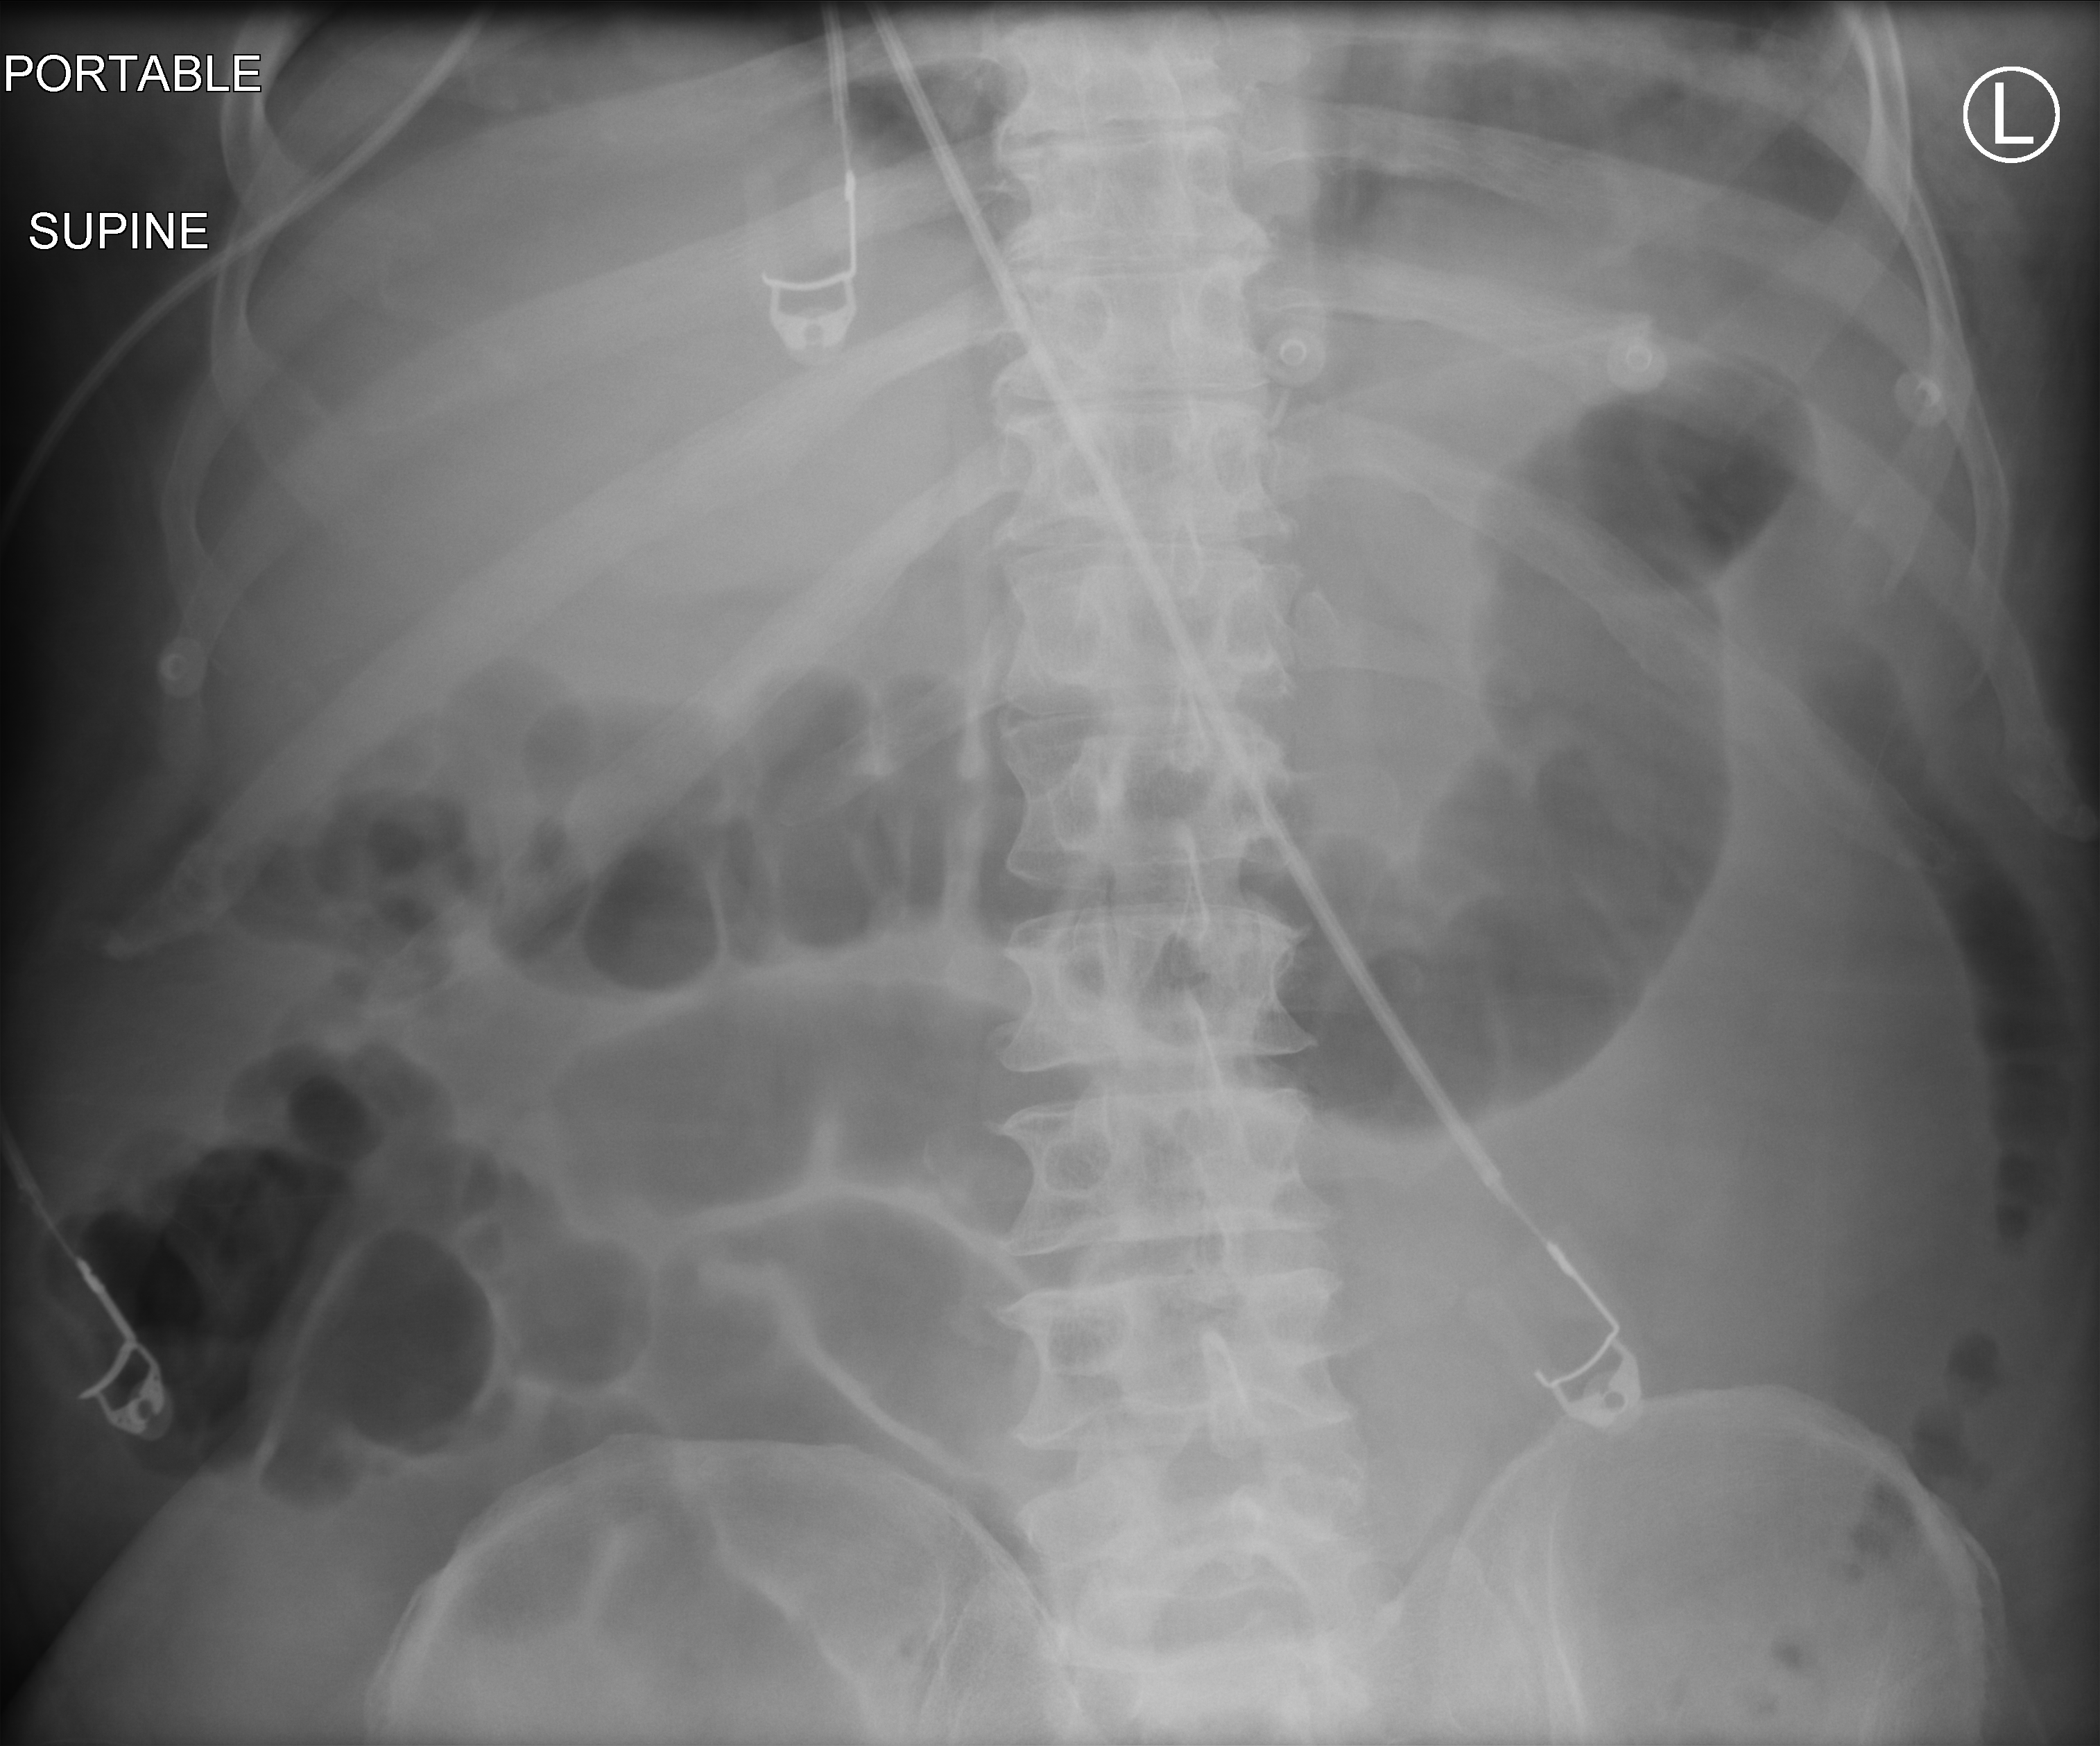
Portable abdomen radiograph. Patient hospitalised with COVID-19; male, aged 18–59 years.
From the hospital-stay record, not from the radiograph (when in the stay this image was taken is not recorded): smoking status (admission record): never; admitted to intensive care during this hospital stay: yes; mechanically ventilated during this hospital stay: yes.